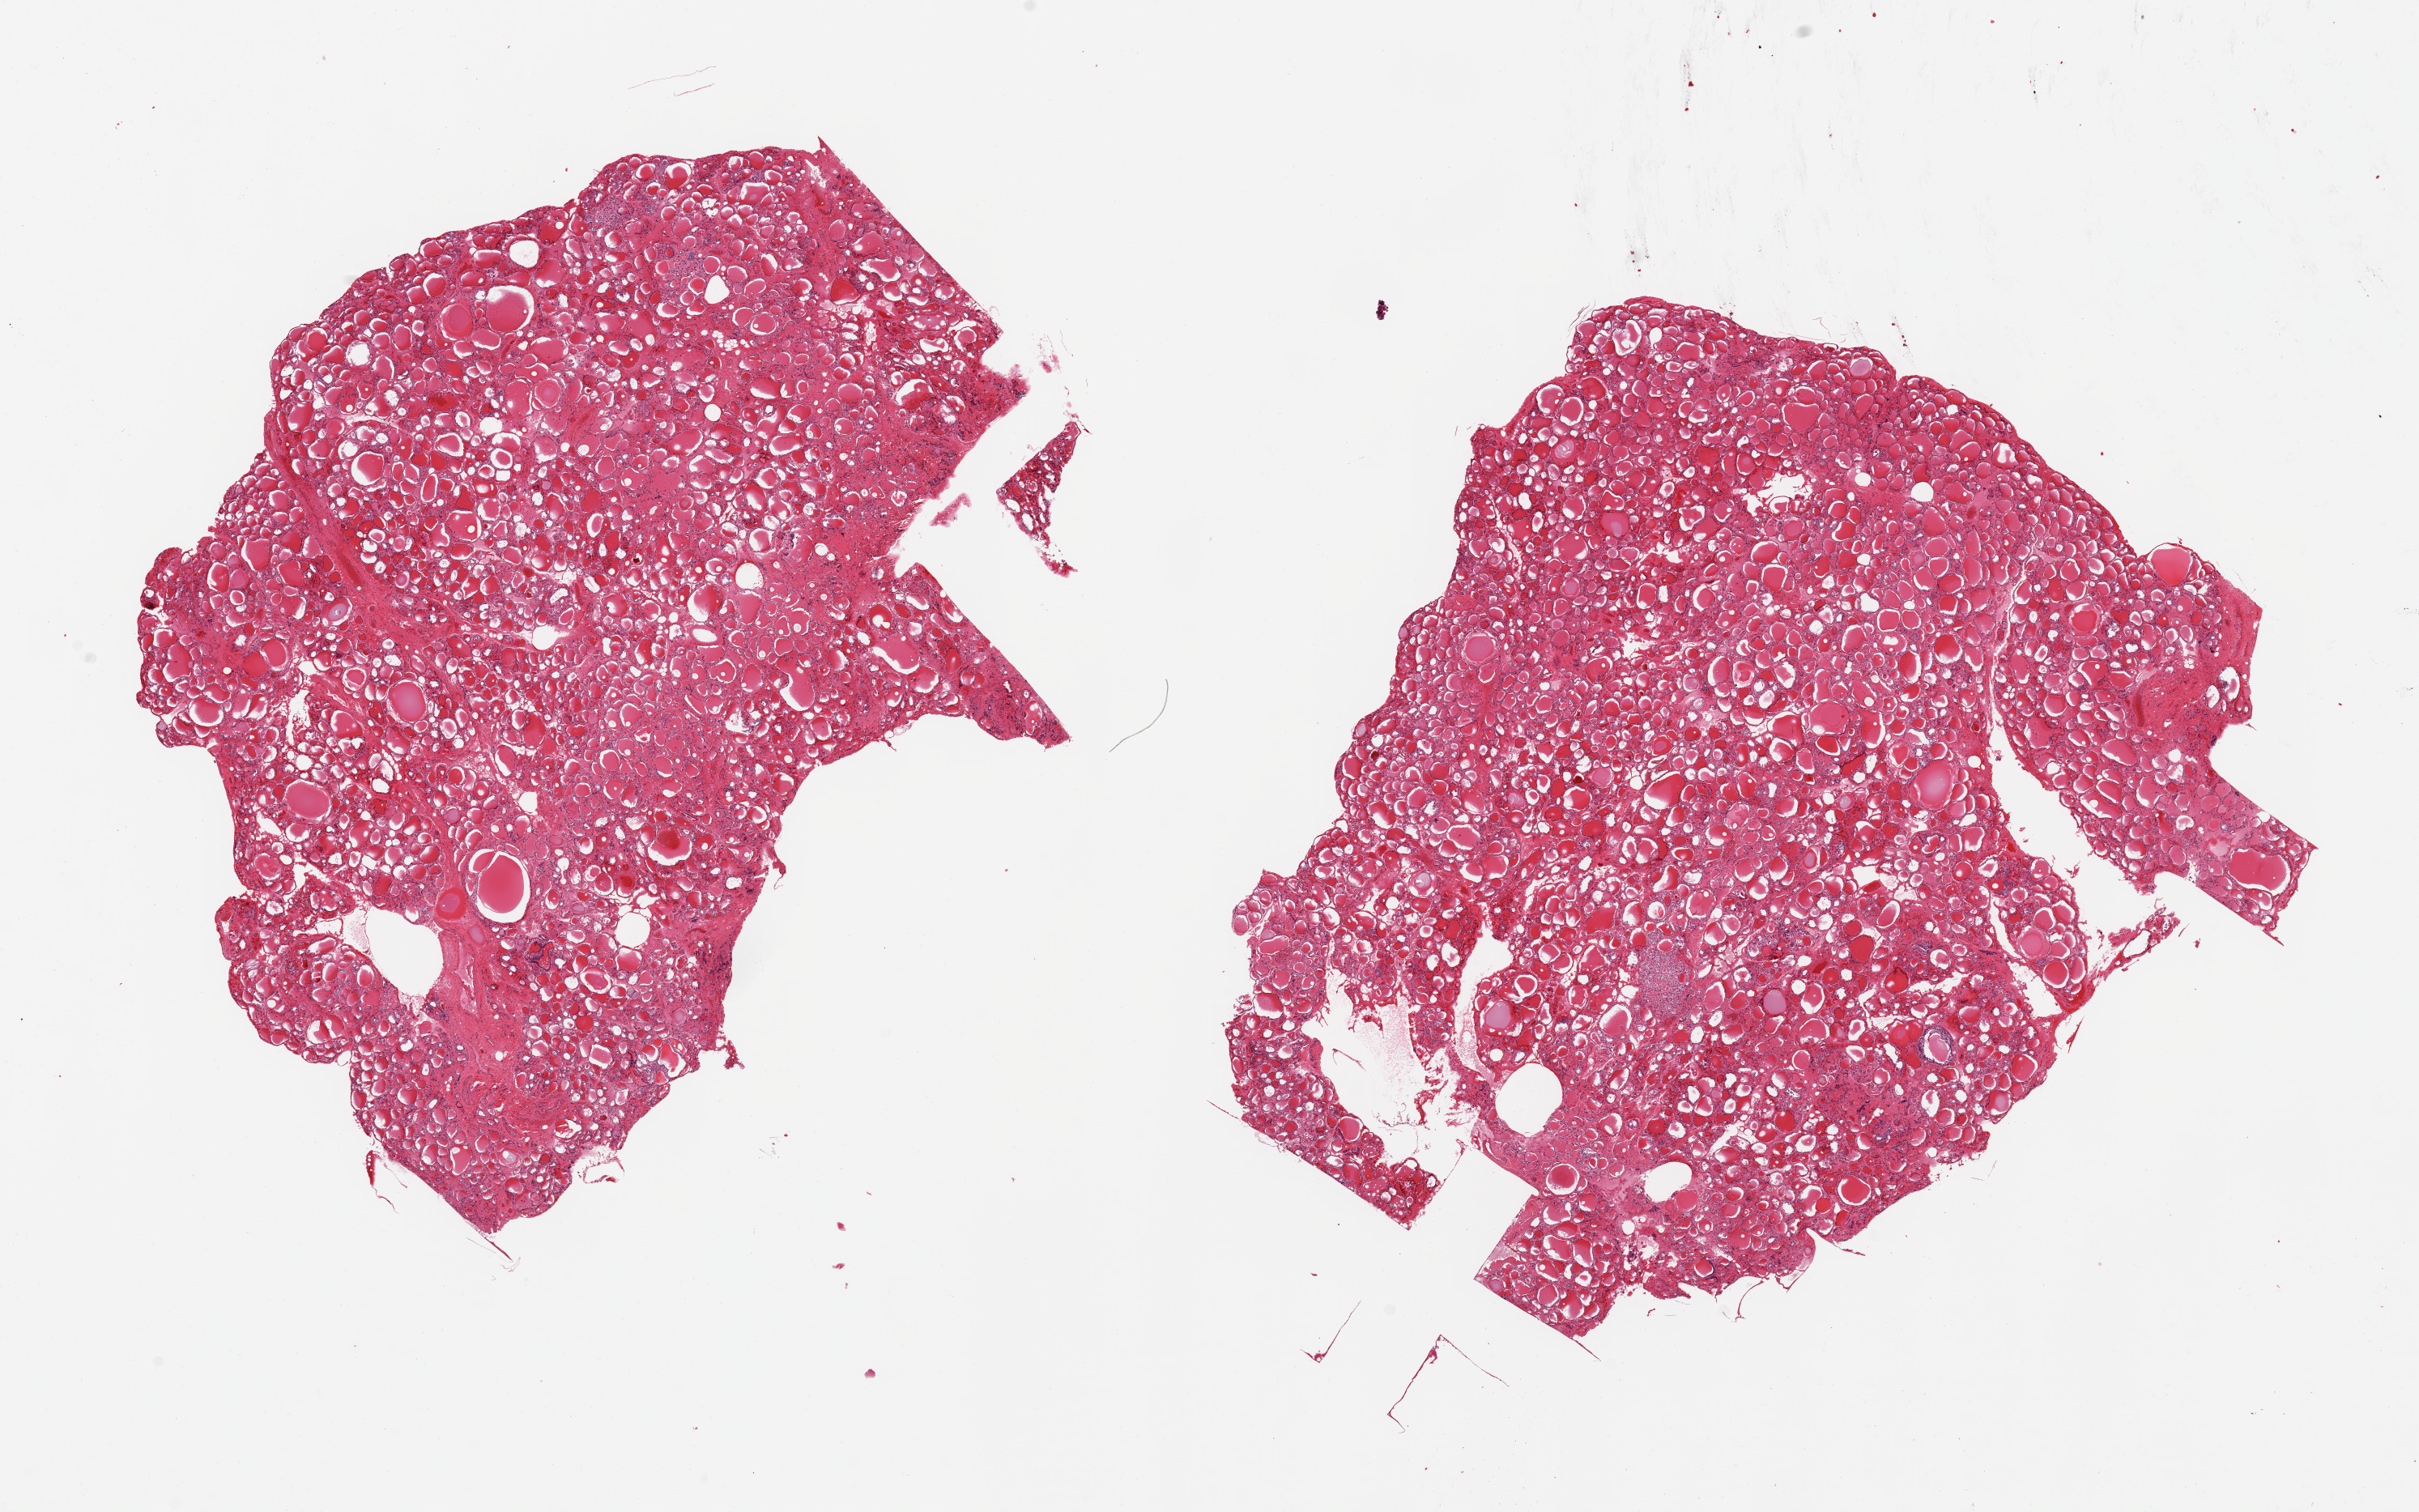
H&E whole-slide image, brightfield, whole scanned area (about 23.6 x 14.8 mm, from a 20x scan) shown as a low-resolution overview, PAXgene-fixed, paraffin-embedded tissue, sampled site (target tissue): thyroid, tissue donor sample. Male donor.
Pathologist's review note for this sample: 2 pieces; interstitial fibrosis.